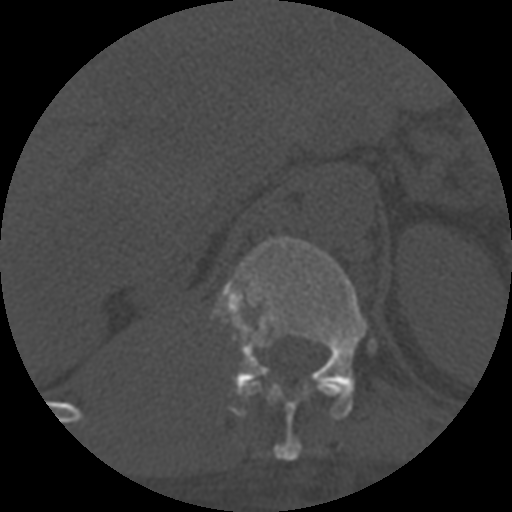
CT including the spine, one axial slice. Position 322 of 708 along the scan axis. Reconstruction kernel STANDARD. 120 kVp. One of 3 acquisitions stored at this slice position. Bone window (W 1800 / L 400 HU). 1.25 mm slice thickness. 512 × 512 image matrix, field of view 160 × 160 mm. Patient age 55 years. From the clinical record (not read from this slice): primary cancer: colon; vertebrae with lytic lesions (as recorded): T12, L1, L5.
Outlined on this slice (semi-automatic segmentation, software-assisted and operator-edited):
- T11 vertebra: bounding box (x1, y1, x2, y2) in pixels: (238, 379, 345, 461)
- T12 vertebra: (214, 236, 367, 420)